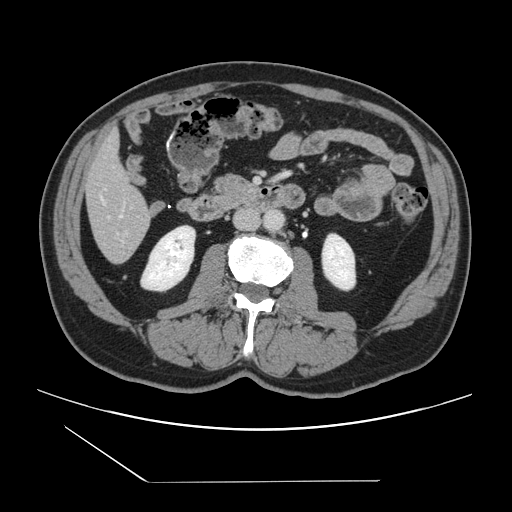
Contrast-enhanced abdominal CT, one axial slice. Slice 37 of 157 in the series (ordered by position). 120 kVp. Intravenous contrast given. Soft-tissue window (W 400 / L 40 HU). 2.5 mm slice thickness. 512 × 512 image matrix, field of view 407 × 407 mm. Male patient, age 61 years. Case-level facts recorded for this patient, not image findings: diagnosis: colorectal cancer liver metastases, imaged before liver resection; multiple liver metastases: yes; largest metastasis: 5.5 cm; disease in both lobes: yes.
Annotated regions visible in this slice (manually delineated by an expert):
- hepatic veins: bounding box <102,198,123,217> (left, top, right, bottom; pixels)
- liver: <85,135,152,263>
- planned liver remnant (the part of the liver to remain after resection): <85,135,148,219>